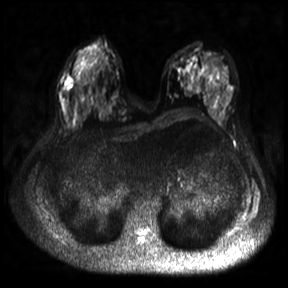
Breast MRI, one axial slice. Slice 14 of 30 in the series (ordered by position). Diffusion-weighted series; image 2 of 4 stored at this slice position (different b-values; order by instance number). 3 T. 4 mm slice thickness. 288 × 288 image matrix, field of view 360 × 360 mm. Female patient.
Annotated regions visible in this slice (outlined manually by an expert reader):
- tumour on diffusion-weighted imaging: bounding box (x1, y1, x2, y2) in pixels: (64, 79, 73, 89)